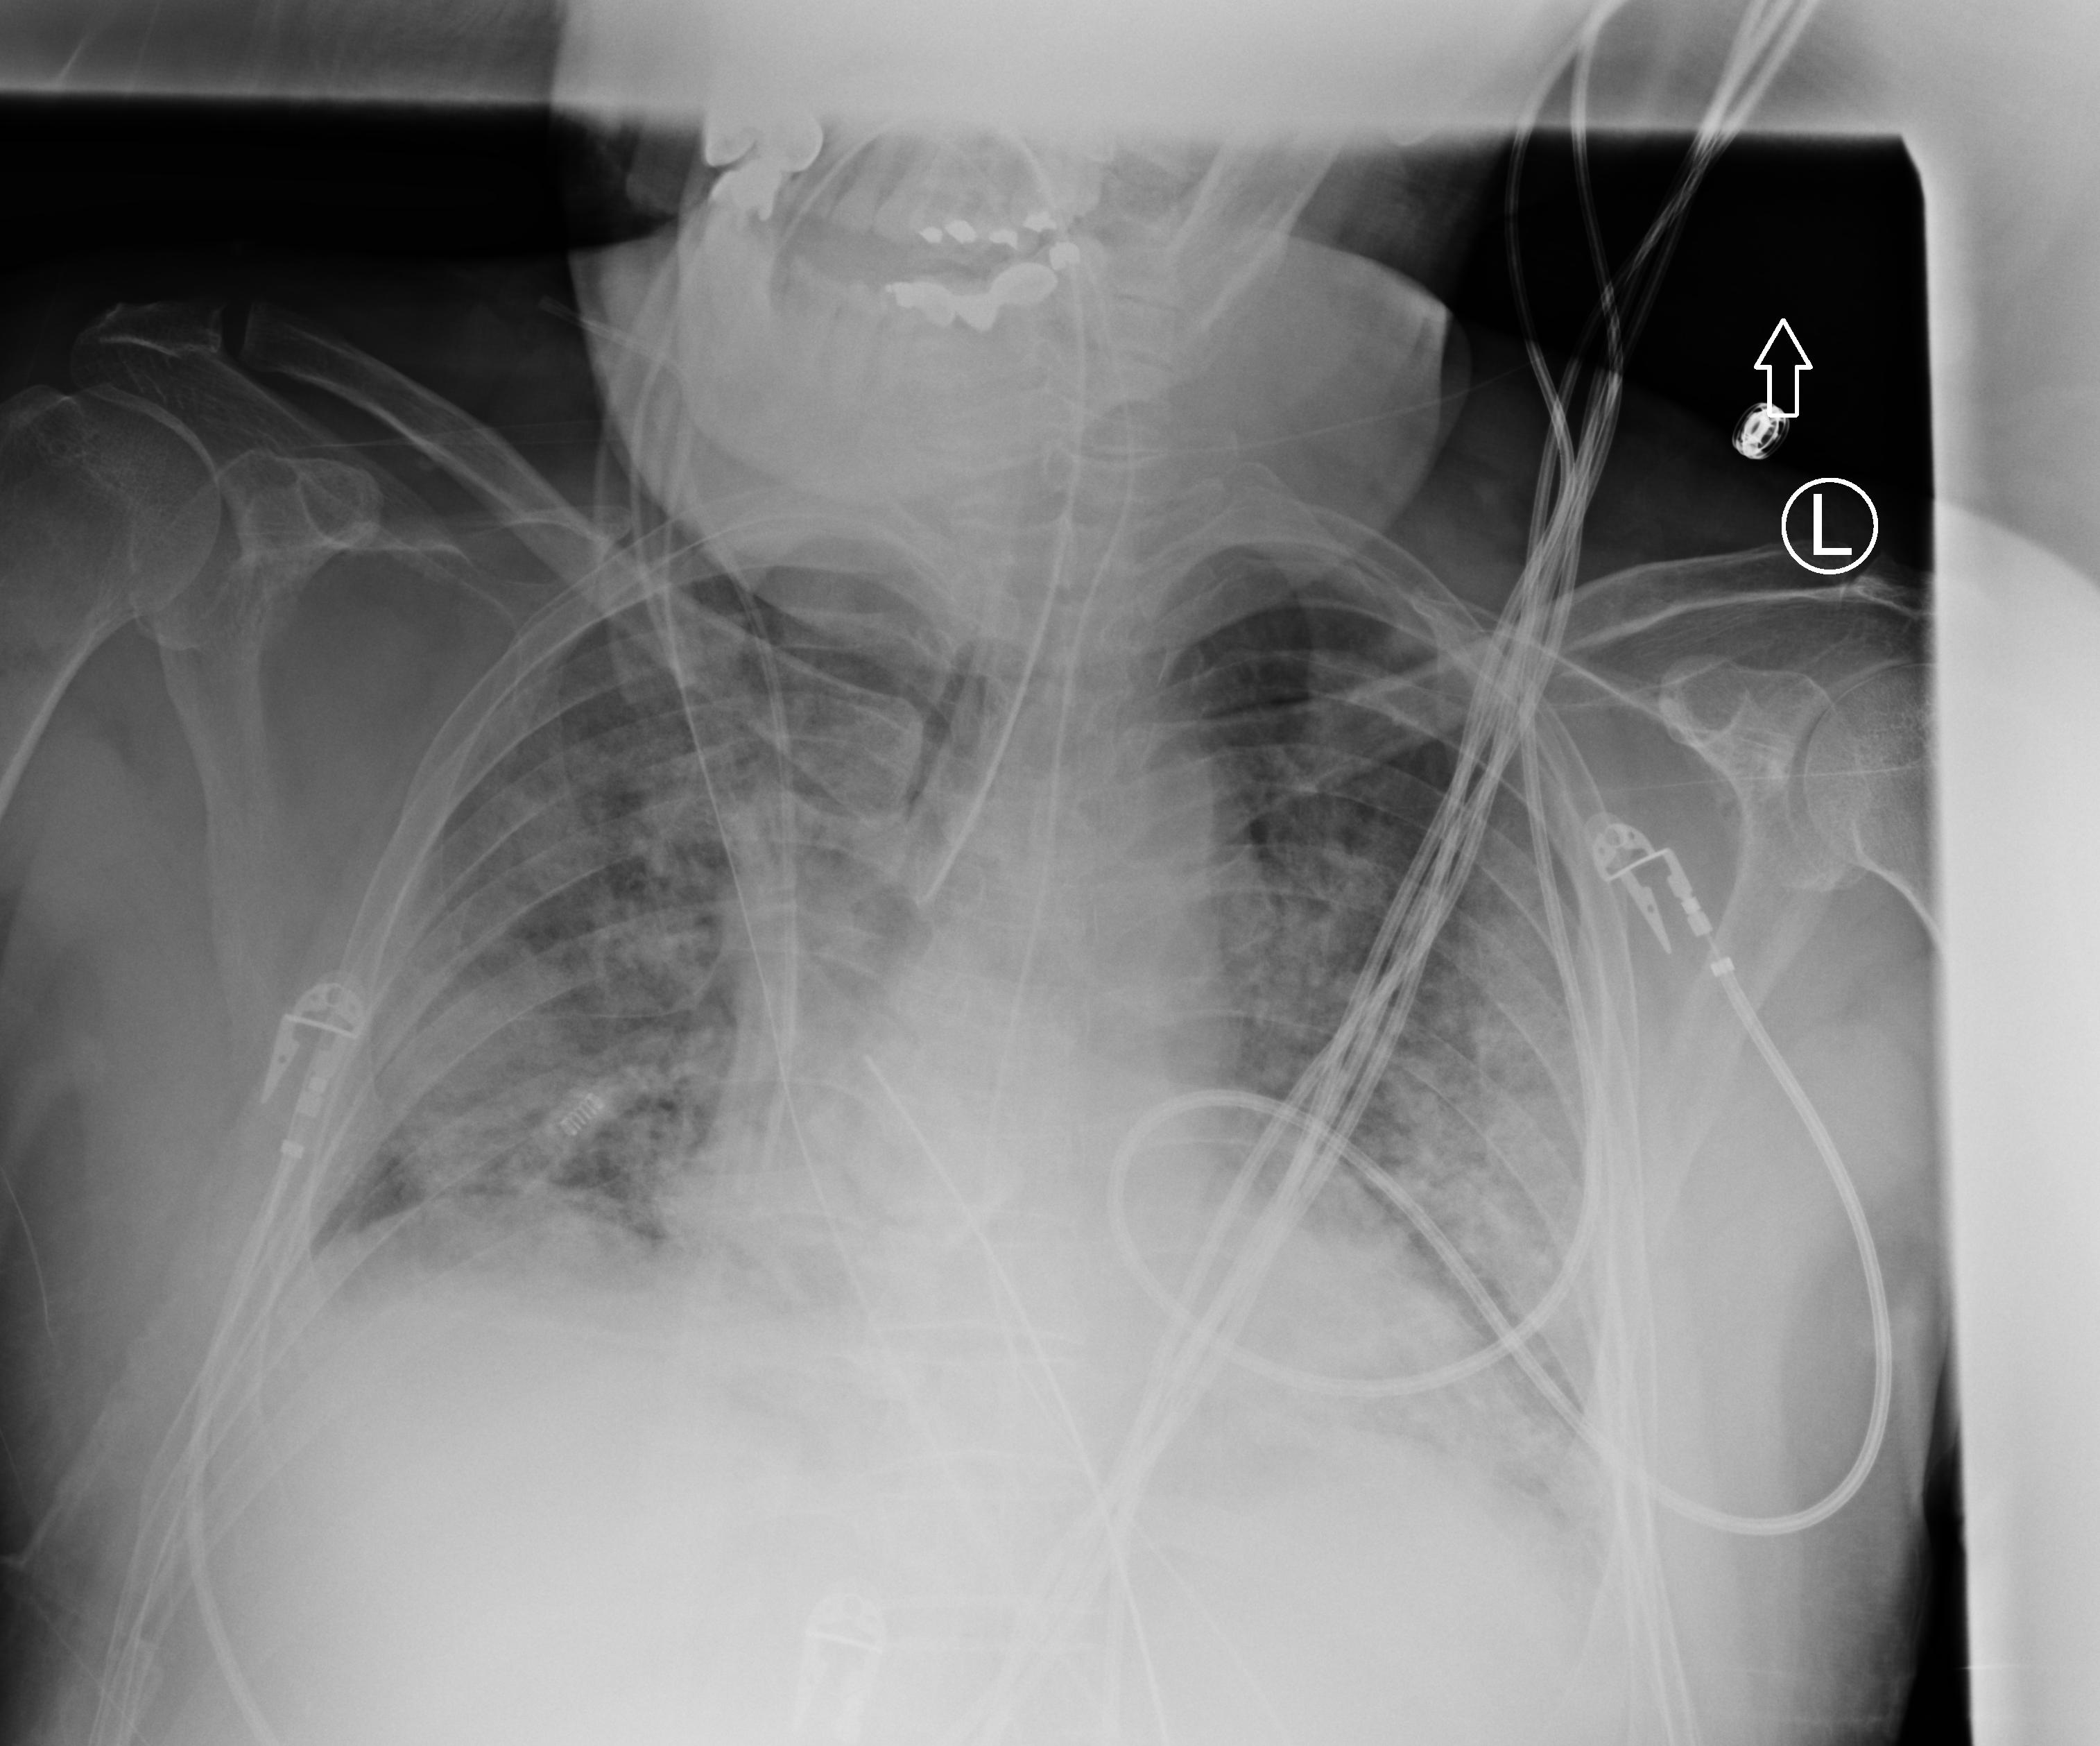
Portable chest radiograph, anteroposterior (AP) projection. Male patient hospitalised with COVID-19, age 60–74 years.
Hospital-stay facts (about this admission, not read from this image; timing relative to this image not recorded):
- chronic kidney disease (admission record): no
- mechanically ventilated during this hospital stay: yes